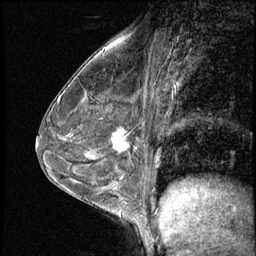
Breast MRI (dynamic contrast-enhanced), one sagittal slice; position 35 of 56 along the scan axis; 3 images stored at this slice position (order not interpretable as contrast timing); 1.5 T; TE 4.2 ms, TR 8.7 ms; 2.5 mm slice thickness; 256 × 256 image matrix. Female patient, age 43 years. Case-level facts recorded for this patient, not image findings: setting: breast cancer imaged before/during neoadjuvant chemotherapy; receptor status: HR-positive, HER2-negative.
Outlined on this slice (semi-automatic segmentation, software-assisted and operator-edited):
- analysis volume of interest (the breast-tissue region the enhancement analysis was run in; not a lesion): bounding box (x1, y1, x2, y2) in pixels: (101, 120, 145, 165)
- tumour enhancement mask (voxels above the 140 % enhancement threshold inside the analysis volume of interest): (112, 129, 130, 152)